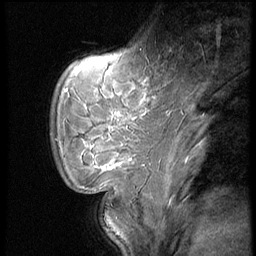
Breast MRI (dynamic contrast-enhanced), one sagittal slice; position 15 of 62 along the scan axis; dynamic contrast-enhanced series, image 2 of 4 at this slice position (ordered by acquisition); 1.5 T; TE 4.2 ms, TR 9 ms; 2.5 mm slice thickness; 256 × 256 image matrix, field of view 180 × 180 mm. Female patient, age 28 years. Case-level facts recorded for this patient, not image findings: setting: breast cancer imaged before/during neoadjuvant chemotherapy.
Outlined on this slice (semi-automatic segmentation, software-assisted and operator-edited):
- analysis volume of interest (the breast-tissue region the enhancement analysis was run in; not a lesion): box from (x=53, y=54) to (x=150, y=183) px
- tumour enhancement mask (voxels above the 140 % enhancement threshold inside the analysis volume of interest): (x=85, y=142)–(x=122, y=169)